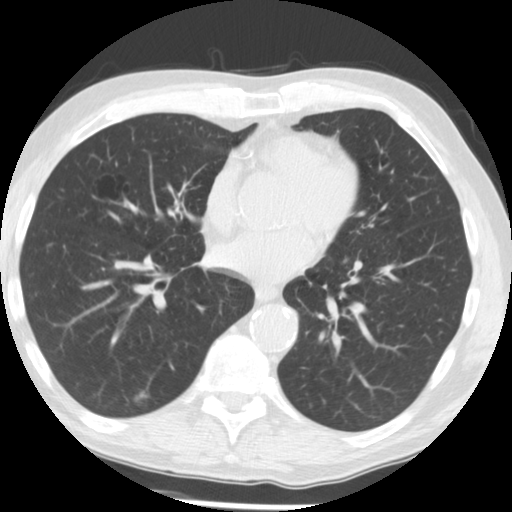
Chest CT (low-dose screening protocol), one axial image. Second screening round (one year after baseline). Lung window (W 1500 / L -600 HU). 2.5 mm slice thickness. Slice 95 of 173 in the series. Male participant, aged 62 years at enrolment.
Expert reader's lesion annotation, bounding box [x1, y1, x2, y2] px = [128, 383, 166, 413]. The screening reader recorded 2 non-calcified nodules or masses ≥4 mm on this exam; which of them this box marks is not recorded. Later outcome: lung cancer diagnosed 506 days after this screen (after the third annual screen) — adenocarcinoma, NOS, right lower lobe, moderately differentiated (G2), stage IIIB (AJCC 6th edition), 15 mm at pathology.